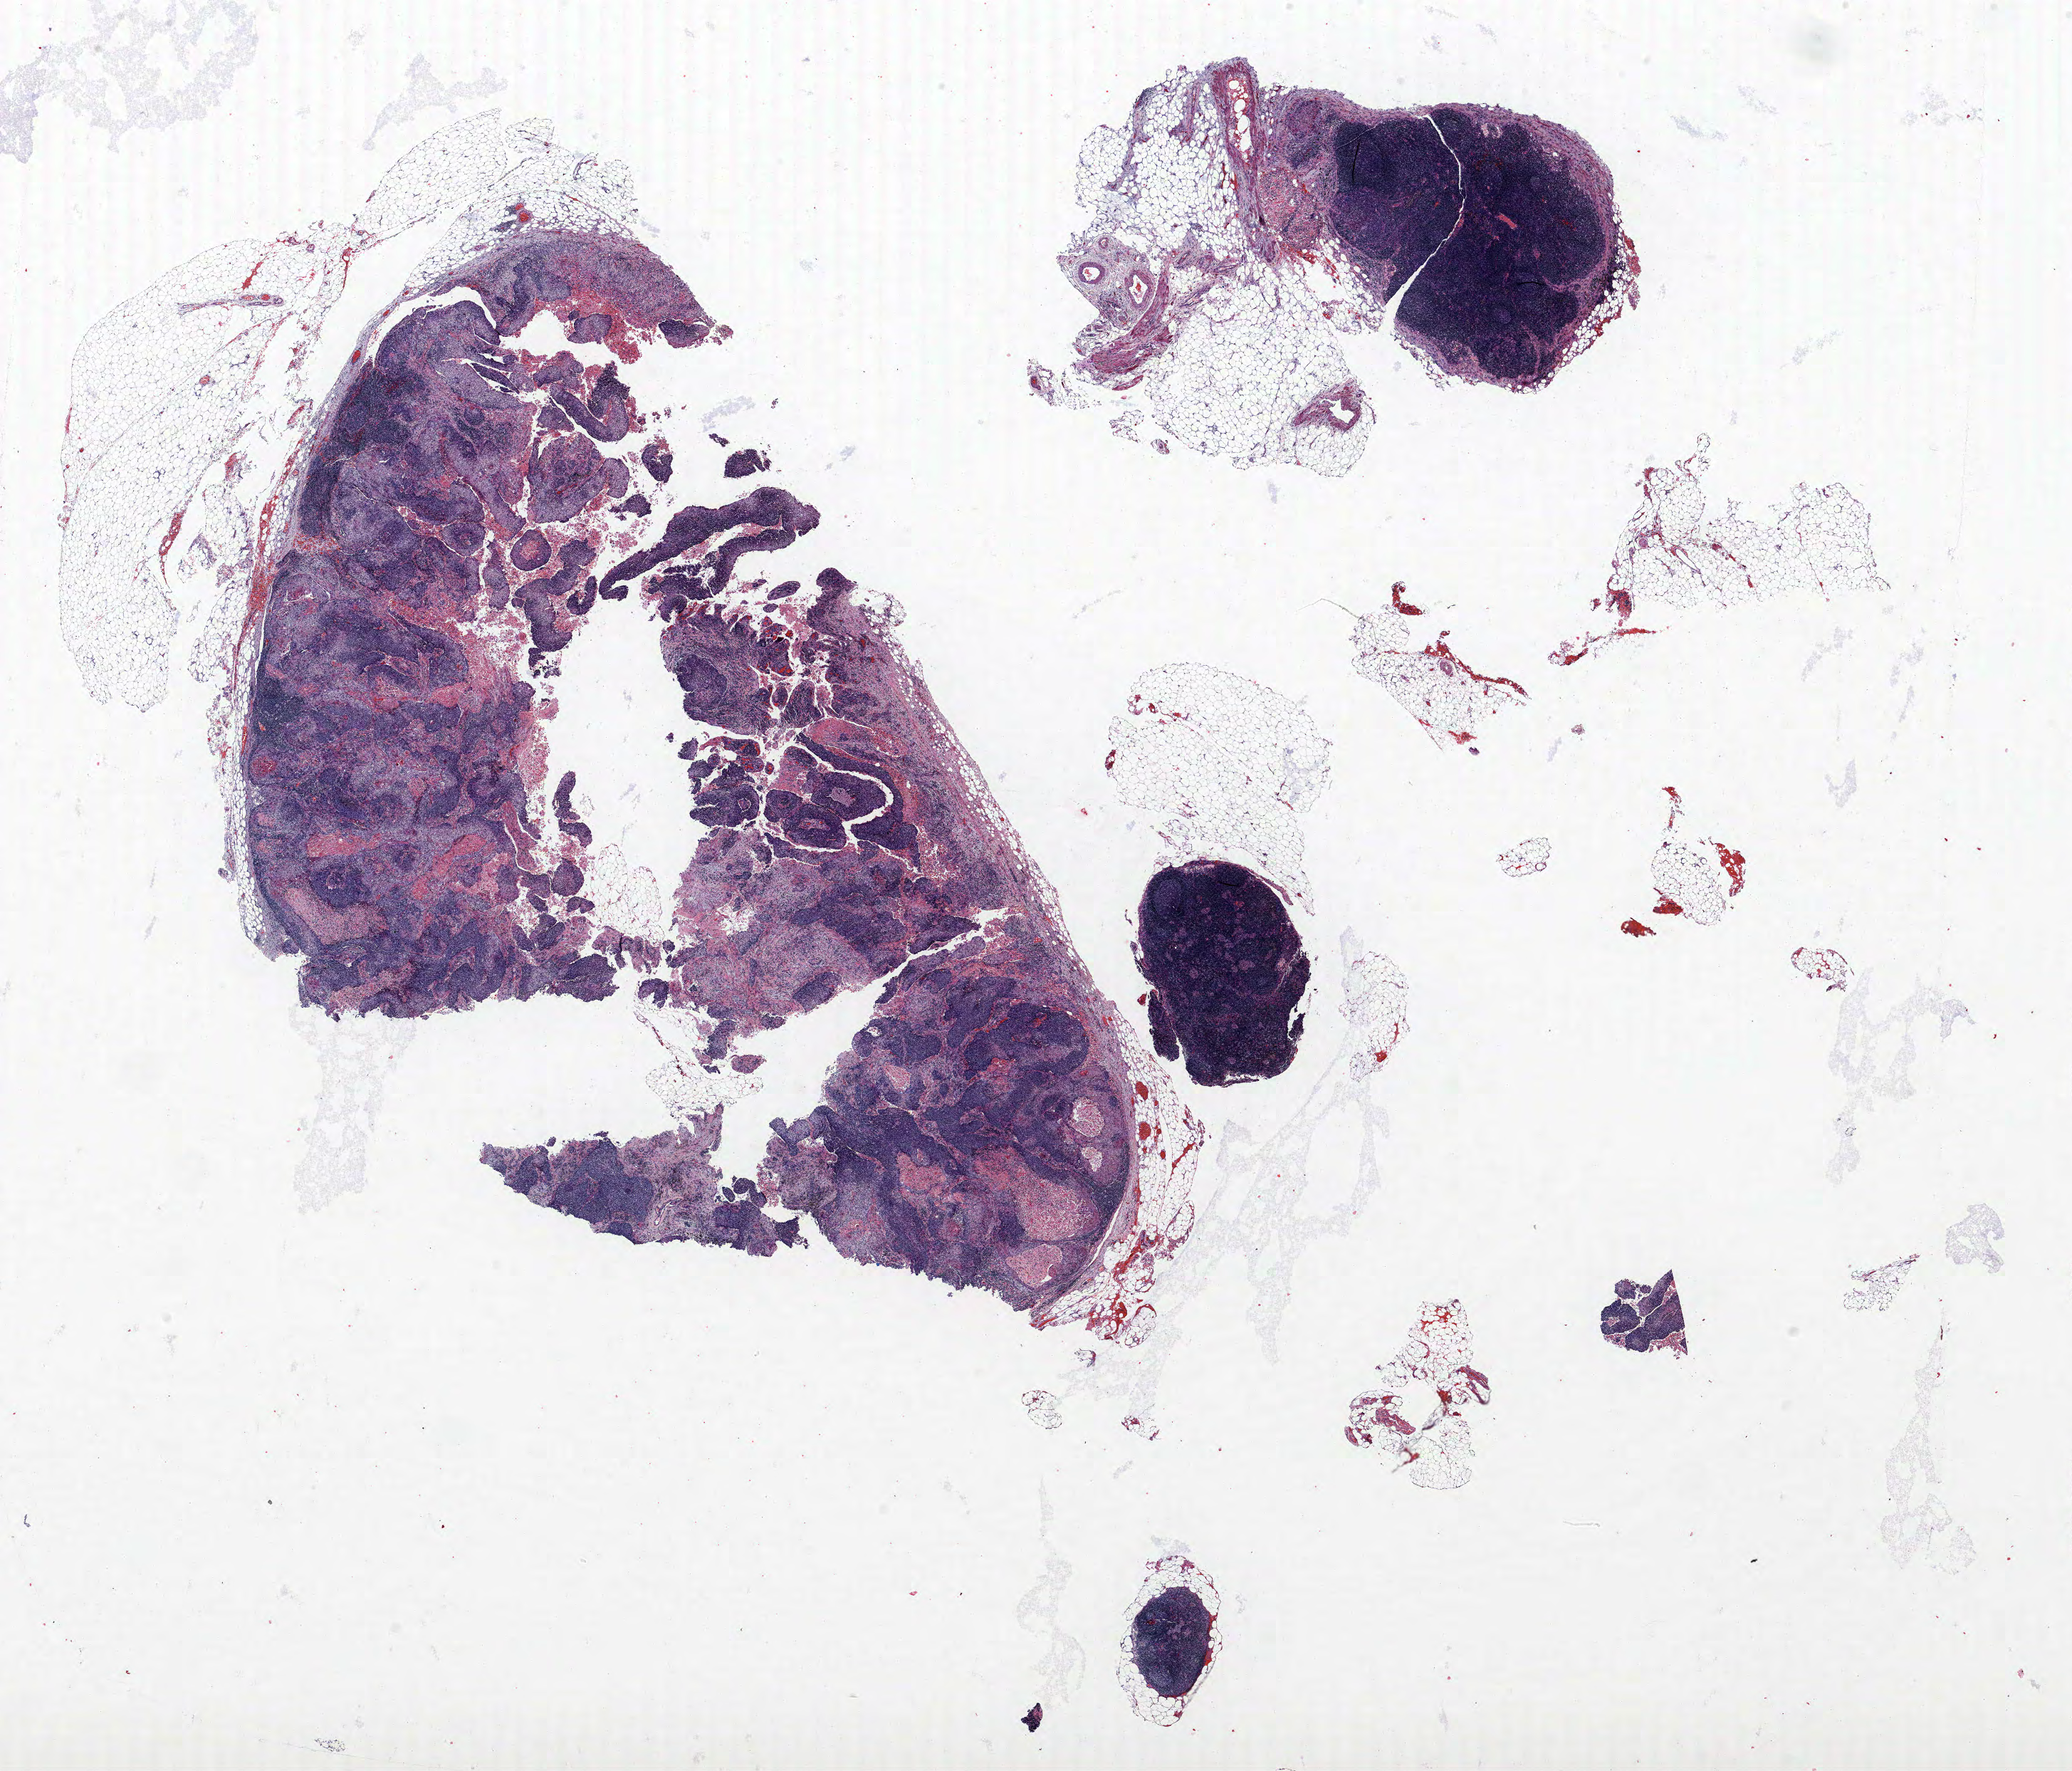
Whole-slide histology image, Hematoxylin and eosin (H&E) stained, a low-resolution overview of the entire scanned area, about 23.3 x 19.9 mm (from a 40x scan); formalin-fixed paraffin-embedded (FFPE) section; lung. Male patient, aged 56 at enrolment. Current smoker at enrolment. Grade: cannot be assessed (GX).
Stage (AJCC 6th edition): IIIA. Primary tumour location (clinical record): left upper lobe. Participant's lung-cancer diagnosis: Squamous cell carcinoma, NOS (ICD-O-3 8070/3). Tumour size (pathology): 30 mm.